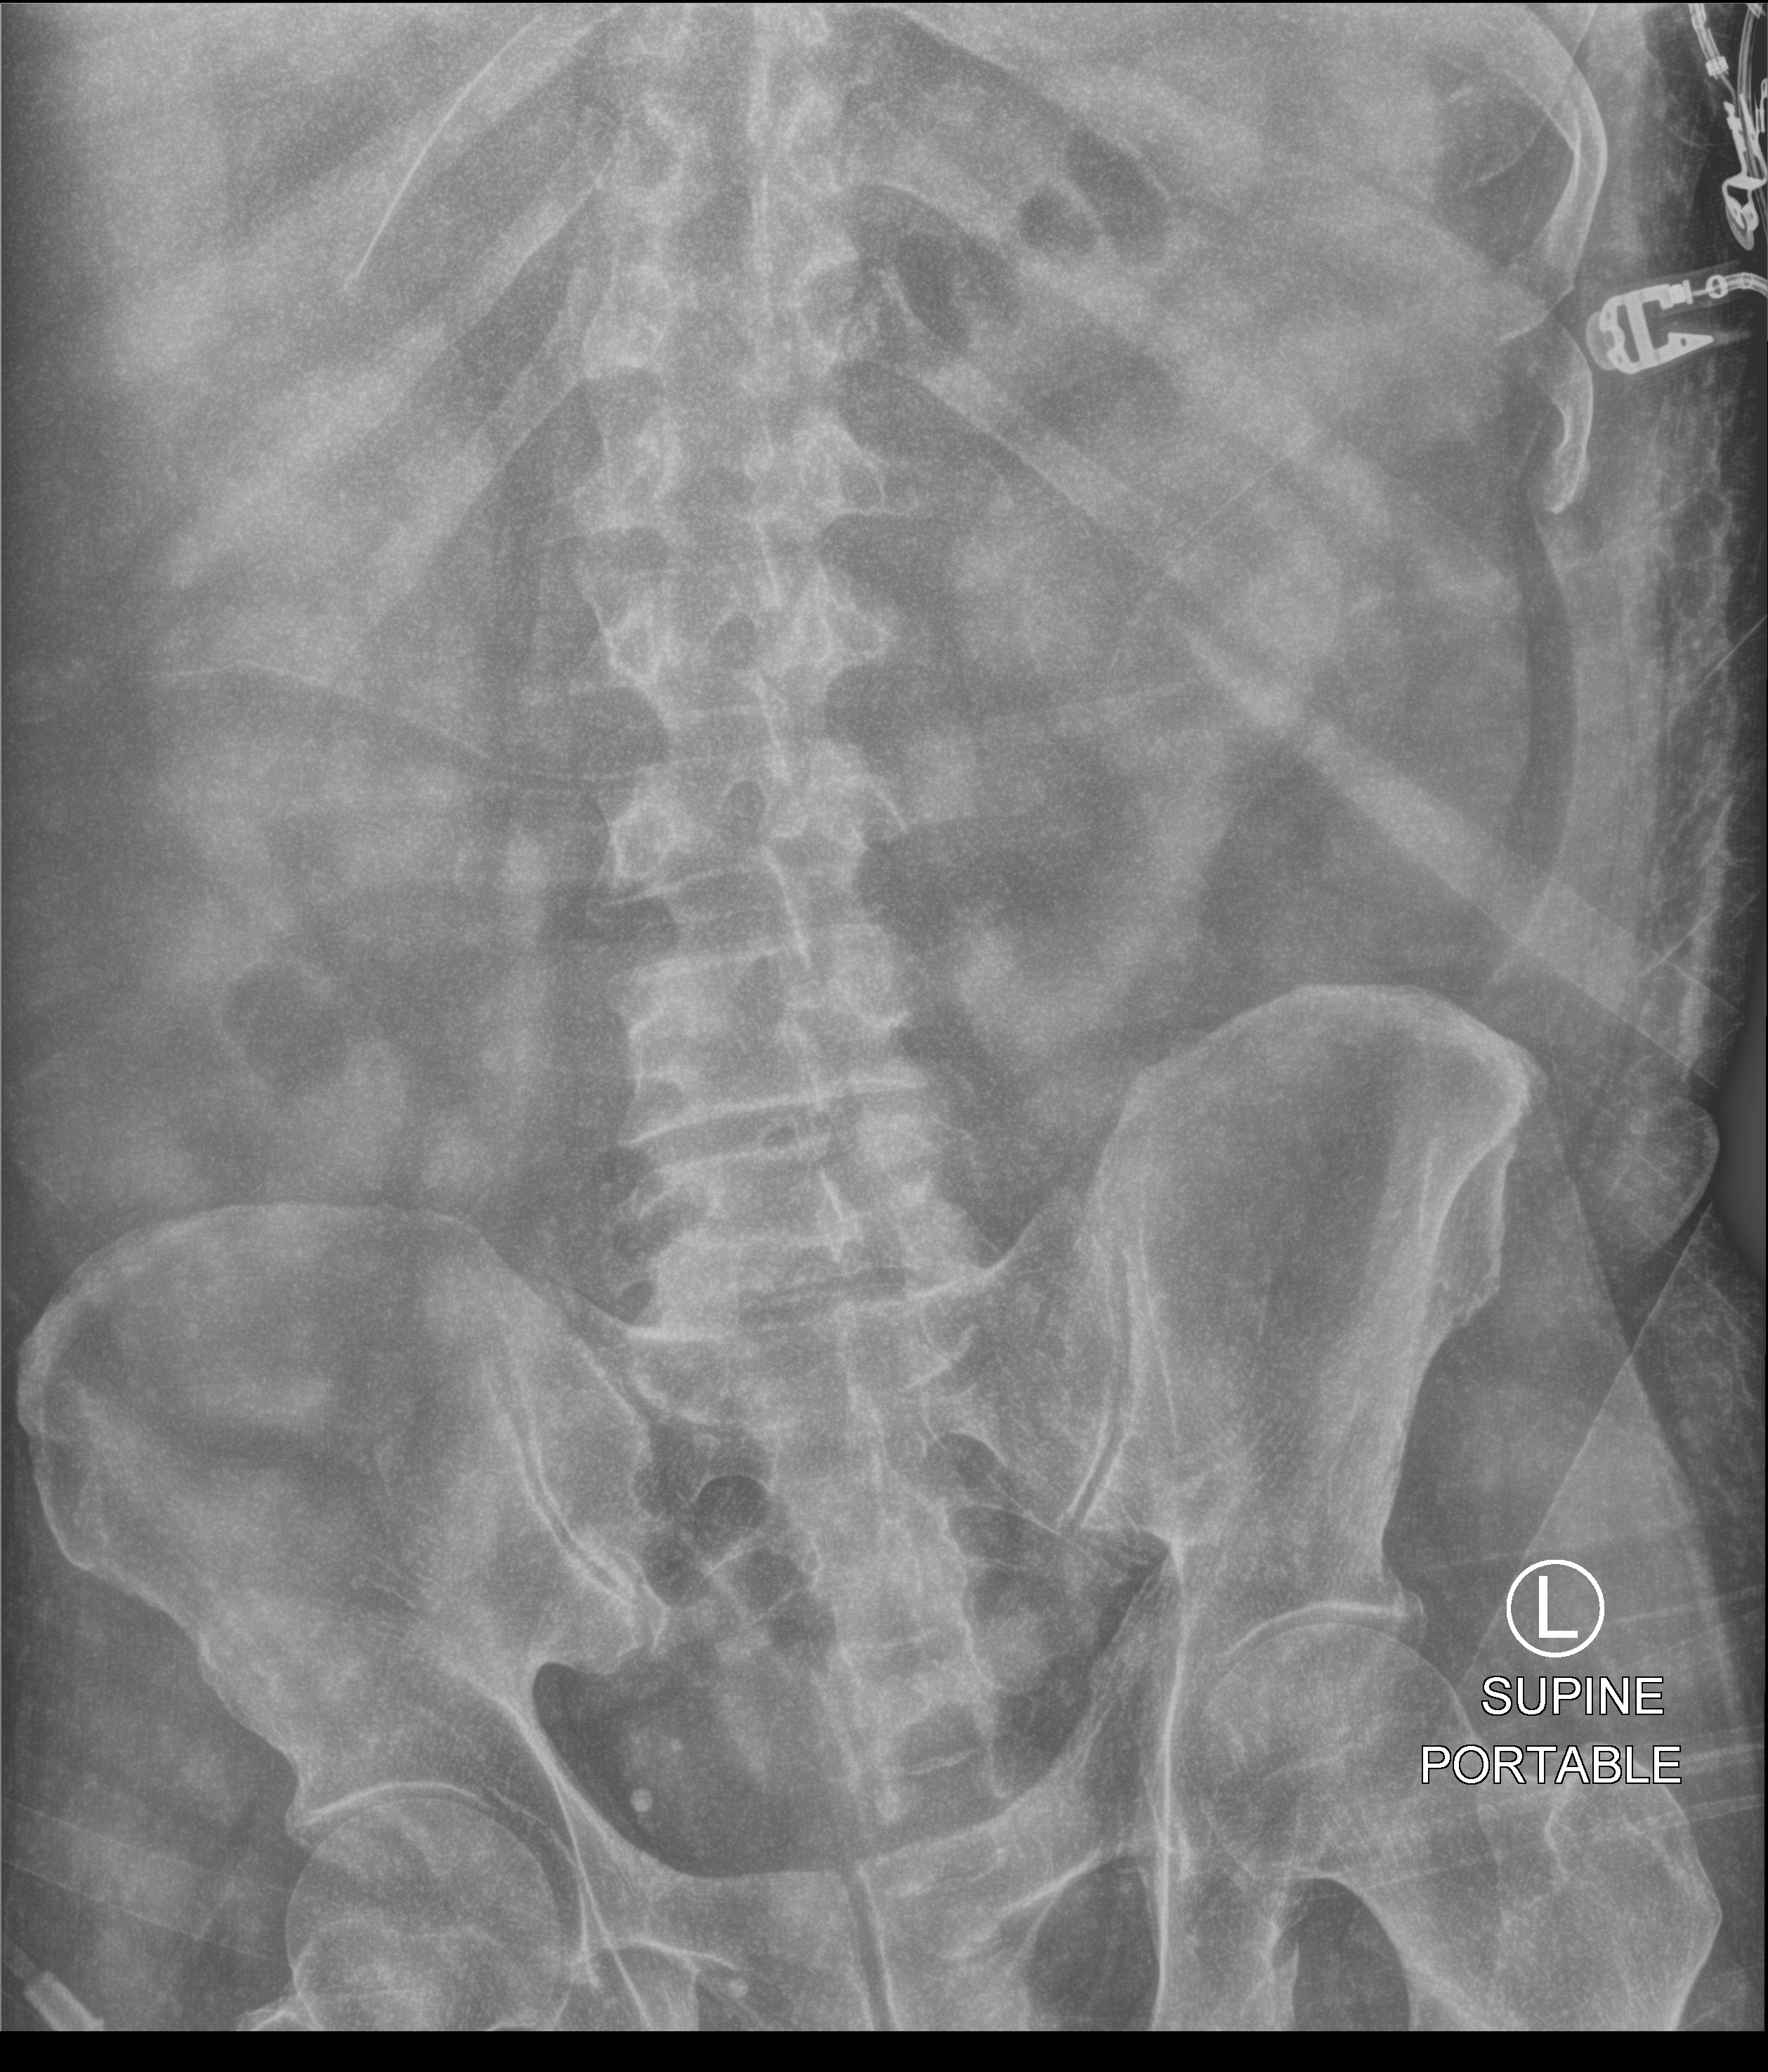
Bedside abdomen radiograph (computed radiography); anteroposterior (AP) projection. Patient hospitalised with COVID-19; male, aged 18–59 years.
Admission-level facts for this patient (not findings on this image; timing relative to this image not recorded):
- mechanically ventilated during this hospital stay: yes